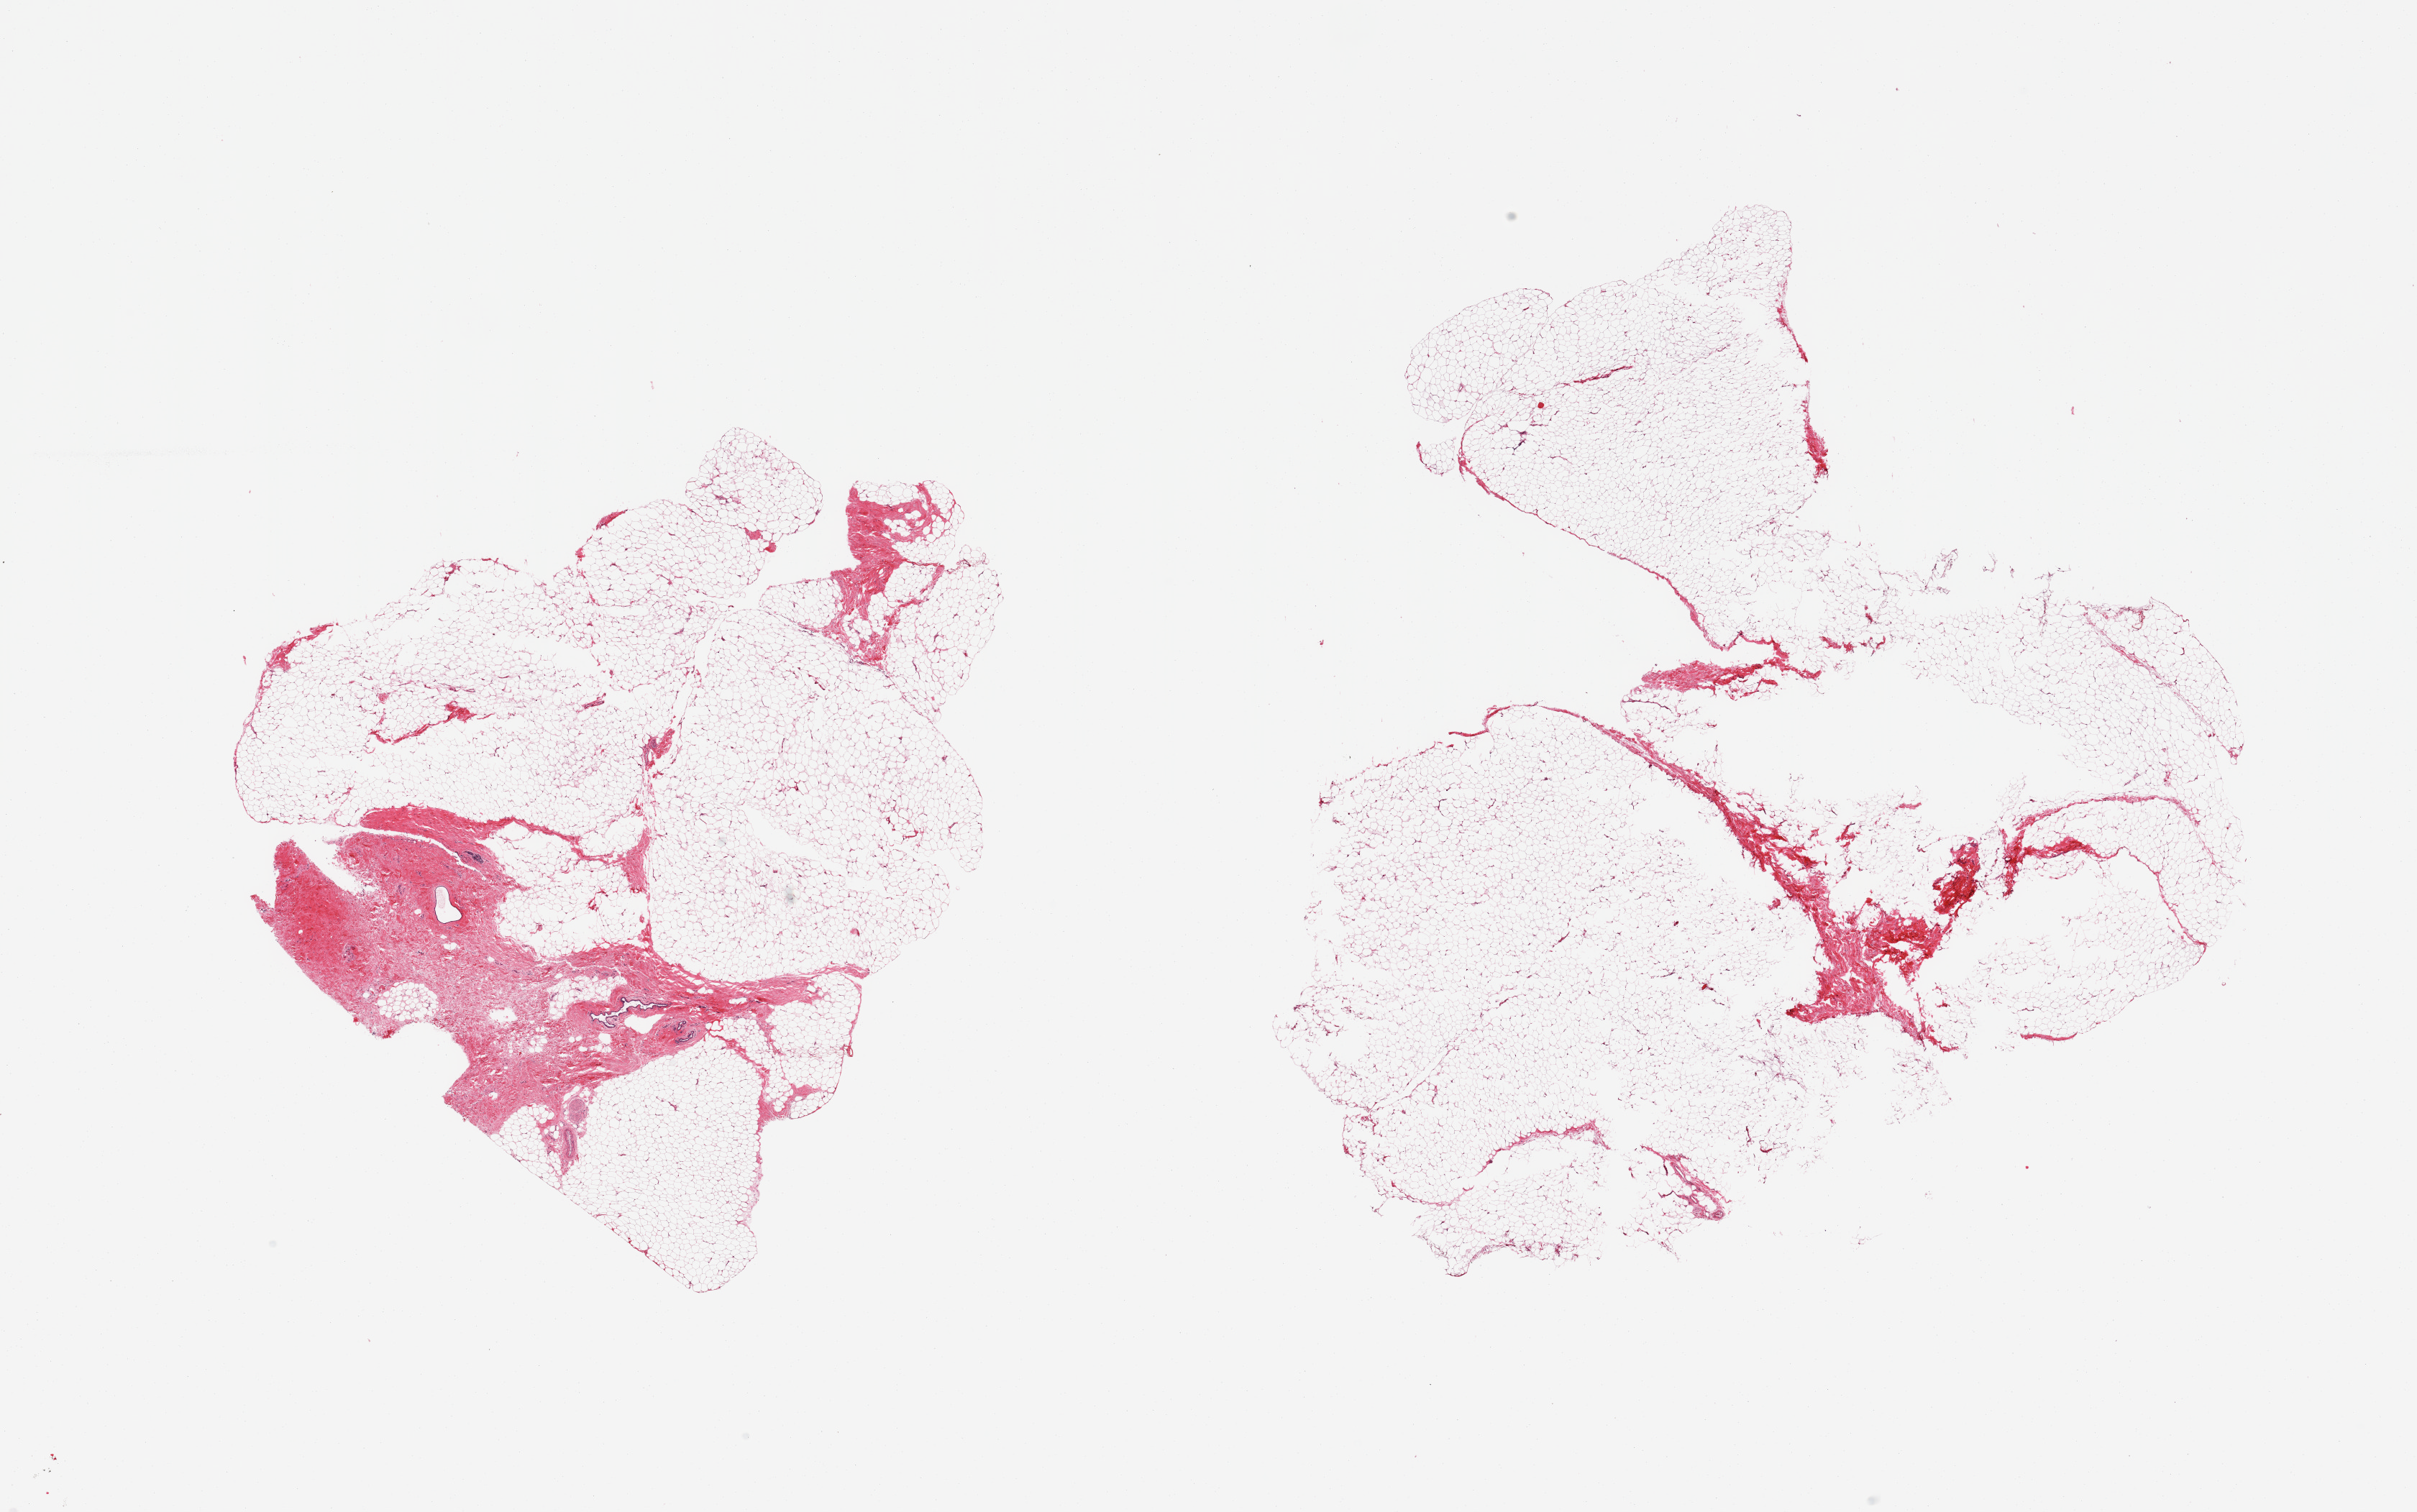
Digitized hematoxylin and eosin (H&E)-stained section, a low-resolution overview of the entire scanned area, about 26.6 x 16.6 mm (slide scanned at 20x). PAXgene-fixed, paraffin-embedded tissue. Section of breast (target tissue). Tissue donor sample.
Pathologist's review note for this sample: 2 pieces; largely fat with 20% fibrous content in 1 piece with a few ducts.